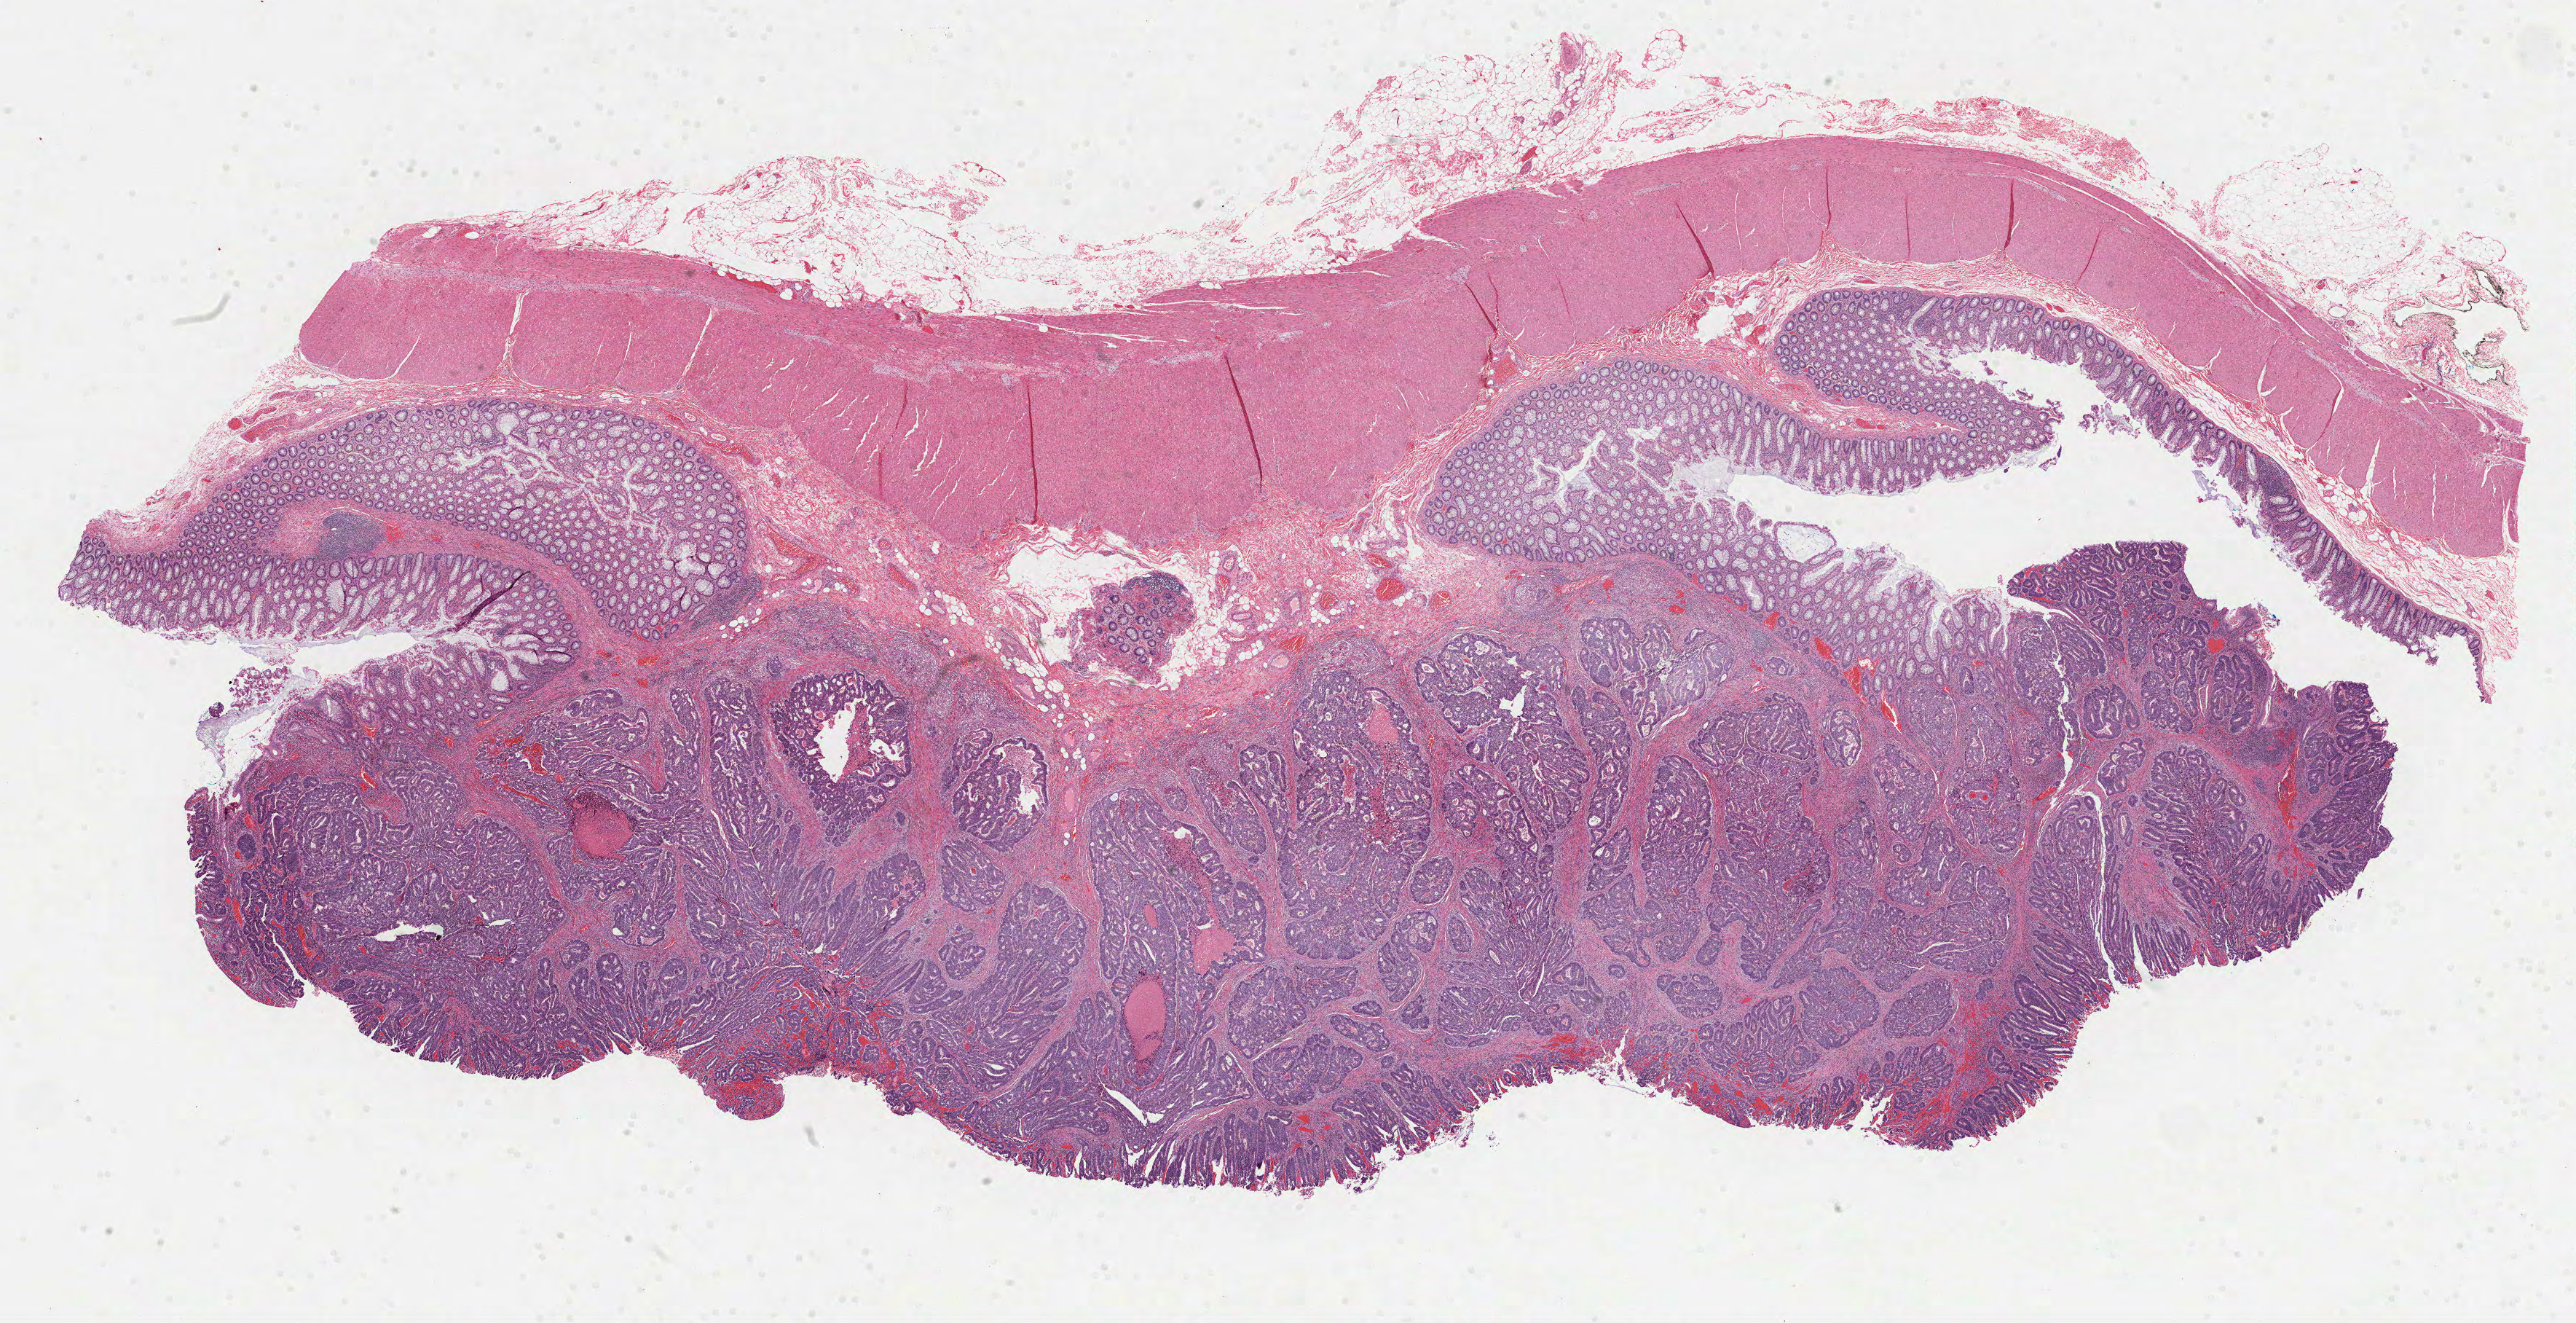
Whole-slide histology image, H&E, a low-resolution overview of the entire scanned area, about 28.5 x 14.6 mm (slide scanned at 40x); formalin-fixed paraffin-embedded (FFPE) diagnostic section; primary tumour sample from the rectum. Male patient; age at initial diagnosis 48 years.
Diagnosis: Adenocarcinoma, NOS (rectosigmoid junction). Lymph nodes positive (case pathology): 0 of 21 examined. AJCC pathologic stage: I (6th edition).